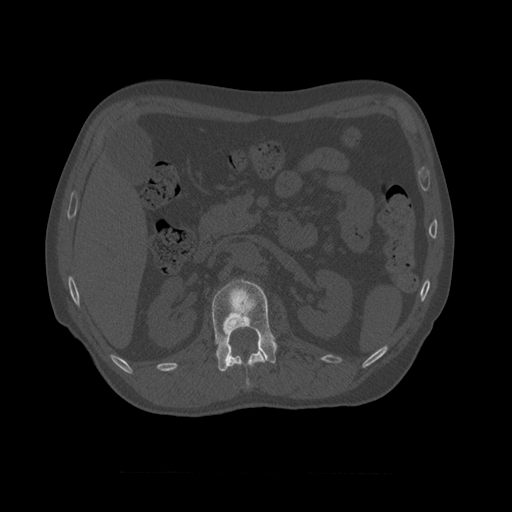
CT including the spine, one axial slice; reconstruction kernel STANDARD; bone window (W 1800 / L 400 HU); 1.25 mm slice thickness; 512 × 512 image matrix, field of view 405 × 405 mm. Patient age 75 years. Case-level facts recorded for this patient, not image findings: primary cancer: prostate.
Annotated regions visible in this slice (semi-automatically segmented with operator editing):
- L1 vertebra: bounding box [x1, y1, x2, y2] px = [212, 279, 278, 372]
- T10 vertebra: [222, 342, 266, 371]
- T11 vertebra: [226, 351, 267, 389]